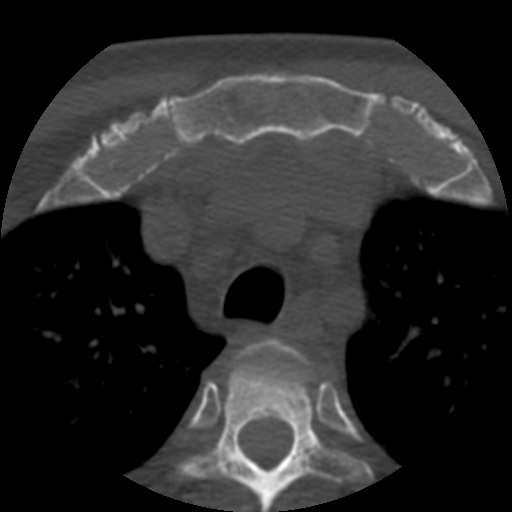
CT including the spine, one axial slice. Slice 416 of 508 in the series (ordered by position). Reconstruction kernel STANDARD. Bone window (W 1800 / L 400 HU). 1.25 mm slice thickness. 512 × 512 image matrix, field of view 160 × 160 mm. Patient age 57 years. Case-level facts recorded for this patient, not image findings: primary cancer: prostate.
Outlined on this slice (semi-automatic segmentation, software-assisted and operator-edited):
- T2 vertebra: bounding box [x1, y1, x2, y2] px = [249, 341, 306, 365]
- T3 vertebra: [182, 345, 372, 512]